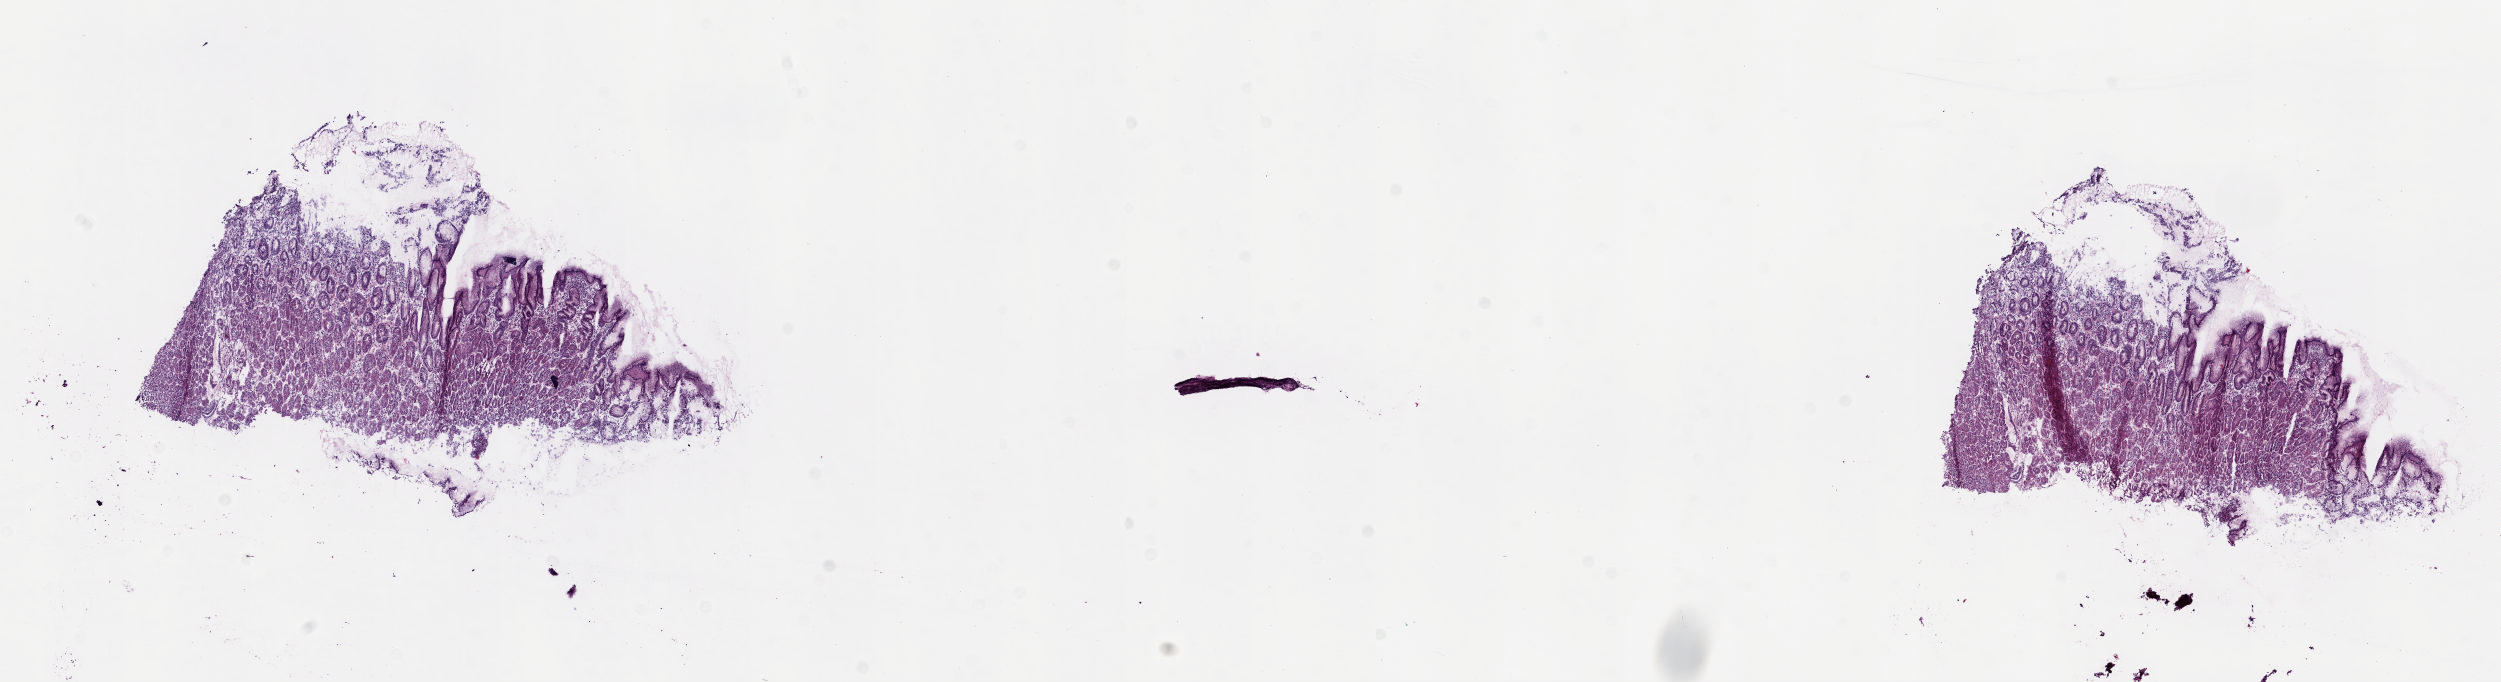
H&E whole-slide image — a low-resolution overview of the entire scanned area, about 19.8 x 5.4 mm (from a 20x scan); frozen section from the top of the tissue portion; sample: solid tissue normal (non-tumour tissue), esophagus. Patient: male, age at initial diagnosis 76 years. Composition of this section per pathologist review: tumour cells 0%, tumour nuclei 0%, normal cells 100%, stromal cells 0%, necrosis 0%. Inflammatory infiltration, as recorded: lymphocyte infiltration 5%, monocyte infiltration 0%, neutrophil infiltration 0%.
• this section: solid tissue normal (non-tumour) sample from the same patient
• patient diagnosis: Adenocarcinoma, NOS (lower third of esophagus)